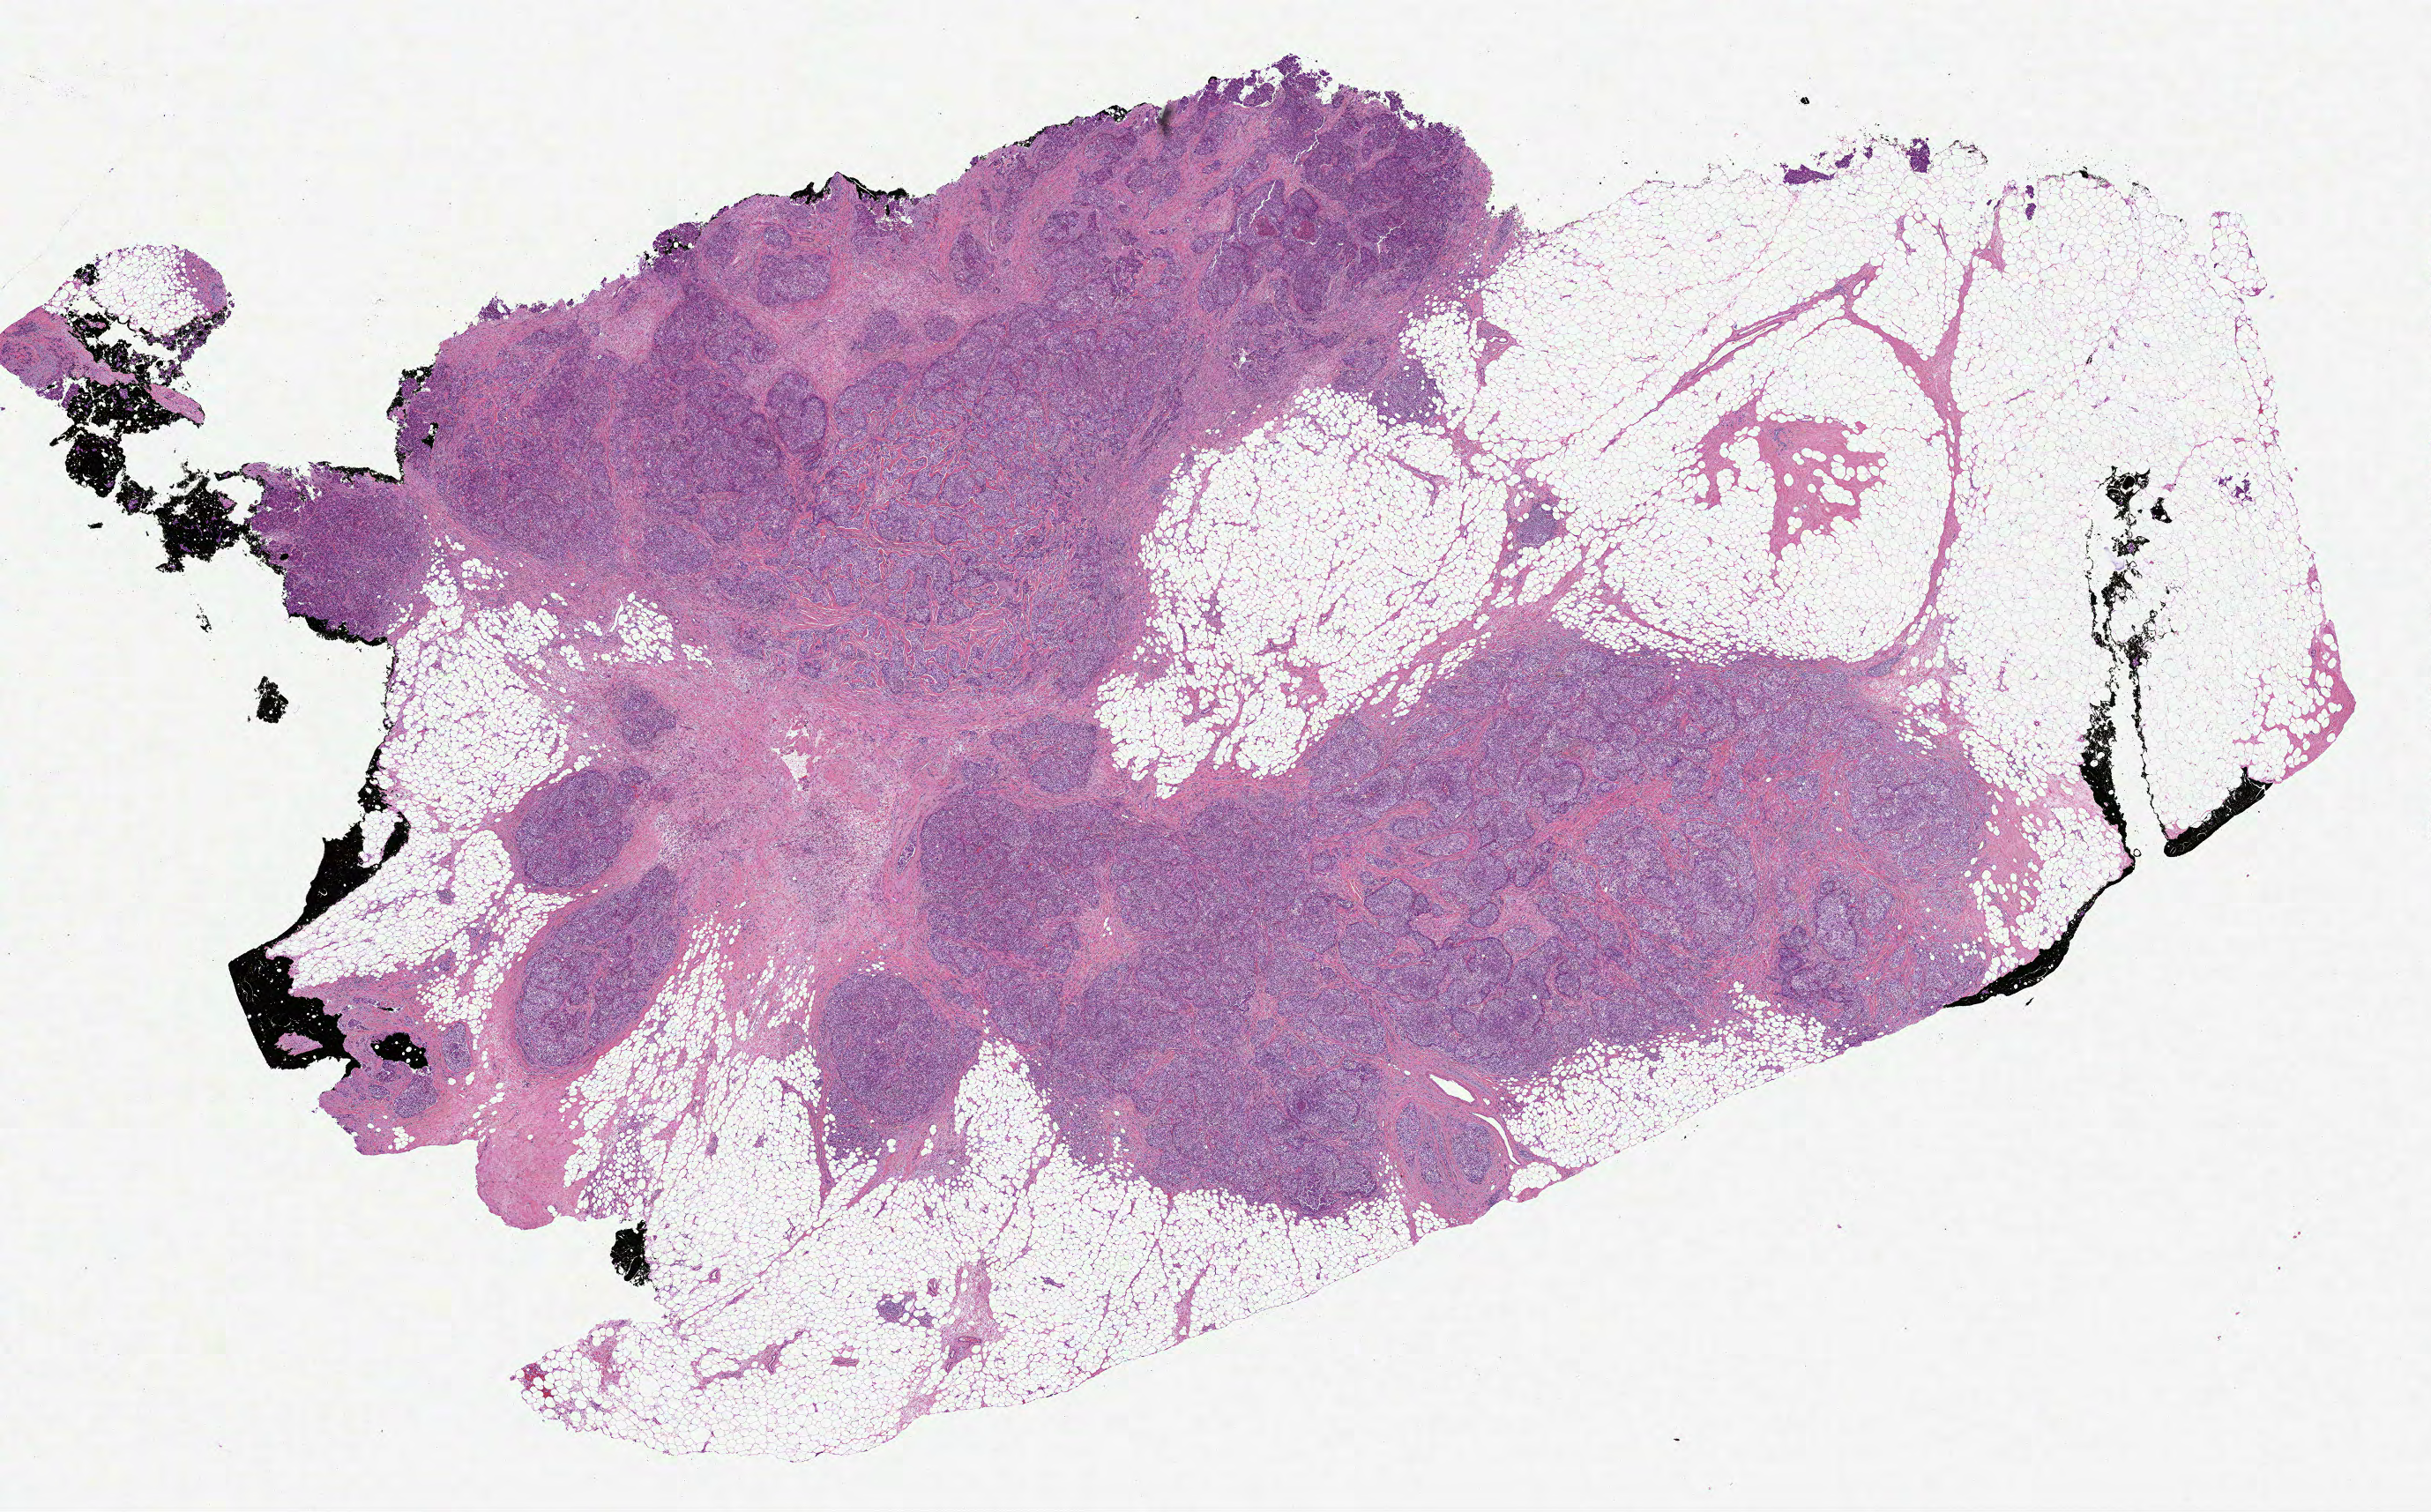
Digitized Hematoxylin and eosin (H&E) stained tissue section (whole slide) — a low-resolution overview of the entire scanned area, about 22.2 x 13.8 mm; formalin-fixed paraffin-embedded (FFPE) diagnostic section; primary tumour sample from the breast. Female, age 41 years at initial diagnosis.
Diagnosis: Infiltrating duct carcinoma, NOS.